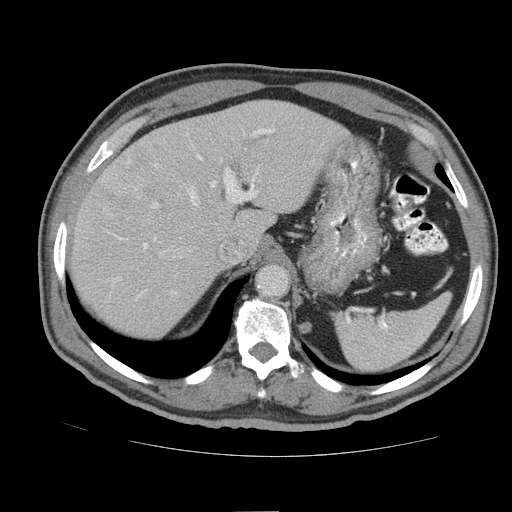
Contrast-enhanced abdominal CT (liver protocol), one axial slice. Slice 64 of 105 in the series (ordered by position). 140 kVp. Soft-tissue window (W 400 / L 40 HU). 2.5 mm slice thickness. 512 × 512 image matrix, field of view 380 × 380 mm. Case-level facts recorded for this patient, not image findings: diagnosis: hepatocellular carcinoma (patient treated with transarterial chemoembolisation; whether this scan precedes or follows treatment is not stated here); TNM stage (as recorded): Stage-IIIB; Child-Pugh class: A; tumour nodularity: multinodular.
Annotated regions visible in this slice (semi-automatically segmented with operator editing):
- liver parenchyma outside the tumour (the mass and vessels are separate outlines, so this box may not span the whole liver): bounding box (x1, y1, x2, y2) in pixels: (68, 100, 350, 336)
- liver vessels: (116, 129, 275, 299)